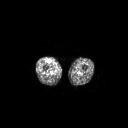
FDG PET of an extremity soft-tissue mass (from a PET/CT study), one axial slice; position 229 of 311 along the scan axis; 3.27 mm slice thickness; 128 × 128 image matrix, field of view 700 × 700 mm. Patient: male, 56 years. From the clinical record (not read from this slice): histological type: pleiomorphic leiomyosarcoma; grade: intermediate; site of the primary tumour: right thigh.
Structures marked on this image (expert contour drawn on MRI and transferred to this co-registered scan by the dataset authors):
- gross tumour volume including surrounding oedema: bounding box [x1, y1, x2, y2] px = [46, 59, 51, 63]